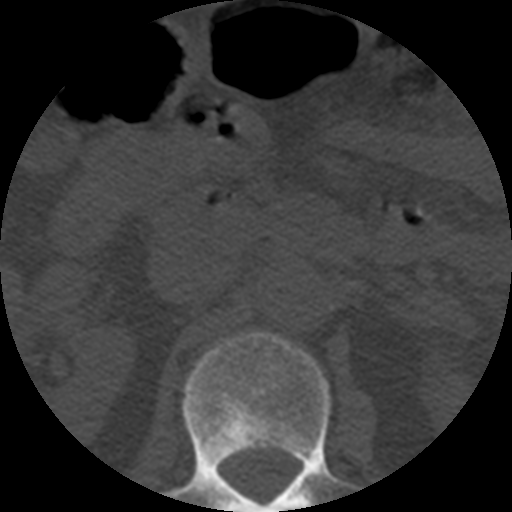
CT including the spine, one axial slice. Position 181 of 508 along the scan axis. Reconstruction kernel STANDARD. 120 kVp. Bone window (W 1800 / L 400 HU). 1.25 mm slice thickness. 512 × 512 image matrix, field of view 160 × 160 mm. Patient age 57 years. Case-level facts recorded for this patient, not image findings: primary cancer: prostate.
Structures marked on this image (semi-automatic segmentation, software-assisted and operator-edited):
- L1 vertebra: bounding box [x1, y1, x2, y2] px = [166, 332, 358, 512]